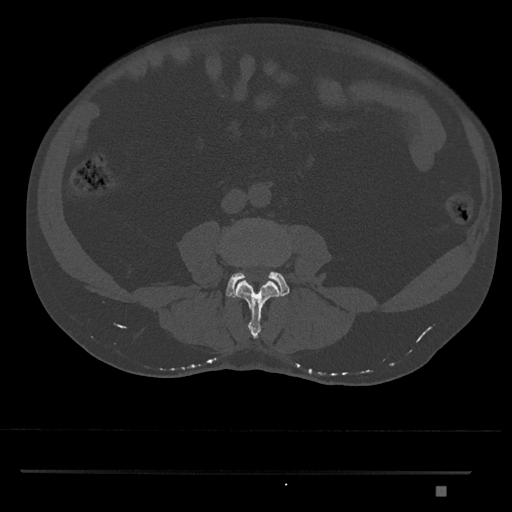
CT including the spine, one axial slice. Position 653 of 1134 along the scan axis. Reconstruction kernel Br40s/3. Bone window (W 1800 / L 400 HU). 512 × 512 image matrix. Patient: male, 65 years. From the clinical record (not read from this slice): primary cancer: prostate.
Structures marked on this image (semi-automatic segmentation, software-assisted and operator-edited):
- L3 vertebra: box from (x=235, y=281) to (x=281, y=339) px
- L4 vertebra: (x=226, y=271)–(x=290, y=298)